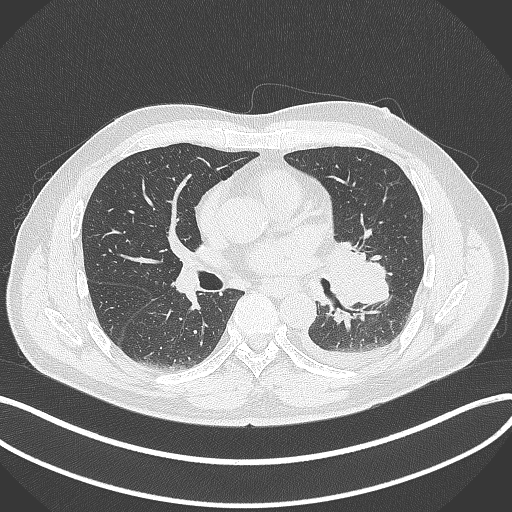
Chest CT, one axial slice; slice 188 of 342 in the series (ordered by position); 120 kVp; lung window (W 1500 / L -600 HU); 1 mm slice thickness; 512 × 512 image matrix, field of view 400 × 400 mm. Male patient, age 58 years. Case-level facts recorded for this patient, not image findings: clinical TNM (as recorded): T3 N1 M1b; histopathological grade: G3.
Outlined on this slice (bounding box drawn by a radiologist):
- lung tumour (recorded histology: small cell carcinoma): bounding box <321,234,394,310> (left, top, right, bottom; pixels)